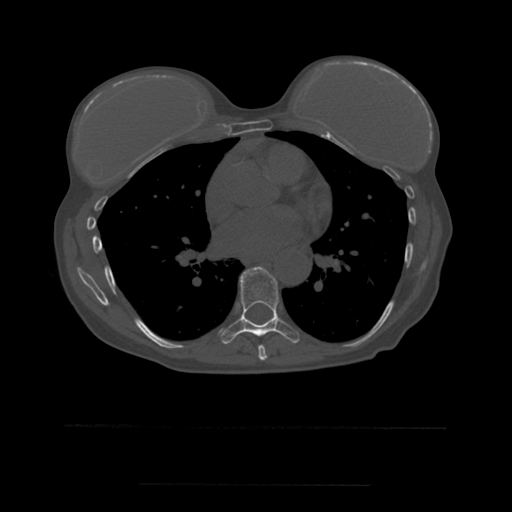
CT including the spine, one axial slice. Position 343 of 544 along the scan axis. Bone window (W 1800 / L 400 HU). 1.25 mm slice thickness. 512 × 512 image matrix, field of view 350 × 350 mm. Patient age 58 years. Case-level facts recorded for this patient, not image findings: primary cancer: lung.
Annotated regions visible in this slice (semi-automatic segmentation, software-assisted and operator-edited):
- T7 vertebra: box from (x=258, y=345) to (x=268, y=361) px
- T8 vertebra: (x=221, y=267)–(x=300, y=344)